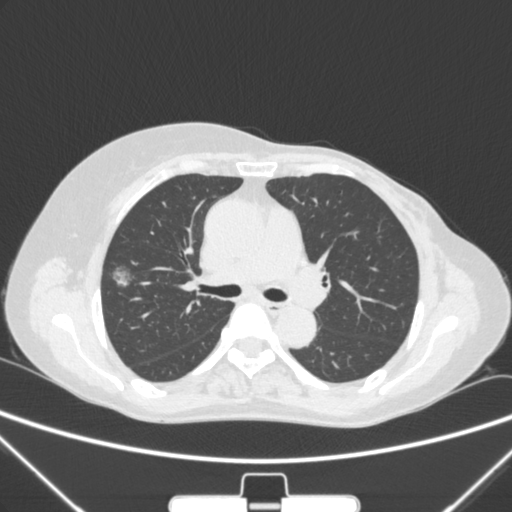
Chest CT, one axial slice. Position 158 of 265 along the scan axis. Lung window (W 1500 / L -600 HU). 1 mm slice thickness. 512 × 512 image matrix, field of view 350 × 350 mm. Patient: female, 64 years. Case-level facts recorded for this patient, not image findings: clinical TNM (as recorded): T1c N0 M0; histopathological grade: G1-2.
Structures marked on this image (rectangle marked by the reading radiologist):
- lung tumour (recorded histology: adenocarcinoma): box from (x=103, y=261) to (x=149, y=299) px